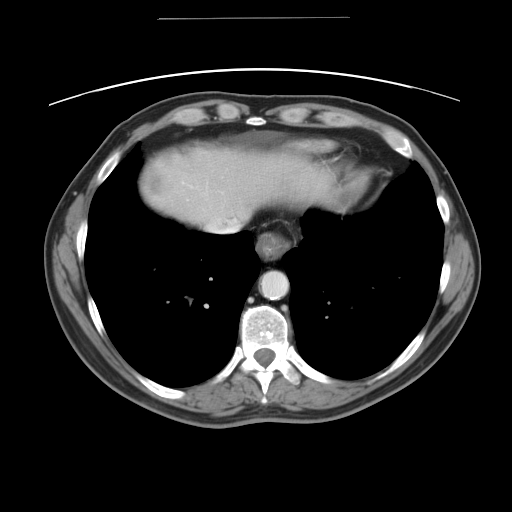
Contrast-enhanced abdominal CT, one axial slice; reconstruction kernel STANDARD; 120 kVp; intravenous contrast given; soft-tissue window (W 400 / L 40 HU); 512 × 512 image matrix, field of view 413 × 413 mm. Male patient, age 57 years. Case-level facts recorded for this patient, not image findings: diagnosis: colorectal cancer liver metastases, imaged before liver resection; multiple liver metastases: yes; largest metastasis: 4 cm; chemotherapy before resection: no.
Outlined on this slice (manually delineated by an expert):
- hepatic veins: bounding box [x1, y1, x2, y2] px = [206, 218, 237, 231]
- liver: [138, 146, 327, 231]
- planned liver remnant (the part of the liver to remain after resection): [206, 146, 328, 231]
- liver metastasis: [143, 170, 165, 198]